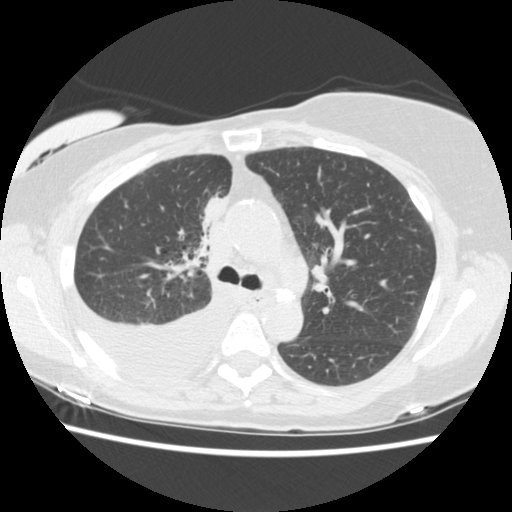
Low-dose screening chest CT, axial slice. Third screening round (two years after baseline). Lung window (W 1500 / L -600 HU). 2.5 mm slice thickness. 120 kVp. Slice 58 of 157 in the series. 512 × 512 image matrix. Female participant, aged 56 years at enrolment. Current smoker at enrolment.
Expert reader's lesion annotation, bounding box <181,187,240,252> (left, top, right, bottom; pixels). The screening reader recorded 2 non-calcified nodules or masses ≥4 mm on this exam (right middle lobe, right lower lobe); which of them this box marks is not recorded.